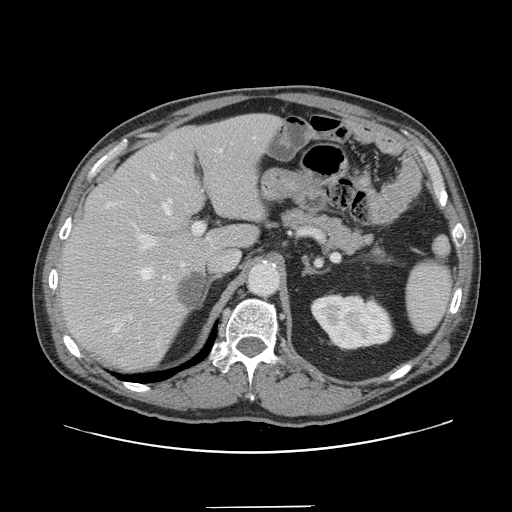
Contrast-enhanced abdominal CT, one axial slice. Slice 96 of 139 in the series (ordered by position). 120 kVp. Intravenous contrast given. Soft-tissue window (W 400 / L 40 HU). 2.5 mm slice thickness. 512 × 512 image matrix, field of view 397 × 397 mm. Male patient, age 64 years. From the clinical record (not read from this slice): diagnosis: colorectal cancer liver metastases, imaged before liver resection; multiple liver metastases: yes; largest metastasis: 3.5 cm; chemotherapy before resection: yes.
Outlined on this slice (outlined manually by an expert reader):
- hepatic veins: bounding box [x1, y1, x2, y2] px = [129, 149, 223, 319]
- liver: [62, 115, 278, 368]
- planned liver remnant (the part of the liver to remain after resection): [62, 115, 270, 368]
- portal vein (with intrahepatic branches): [133, 222, 205, 267]
- liver metastasis: [177, 269, 204, 311]